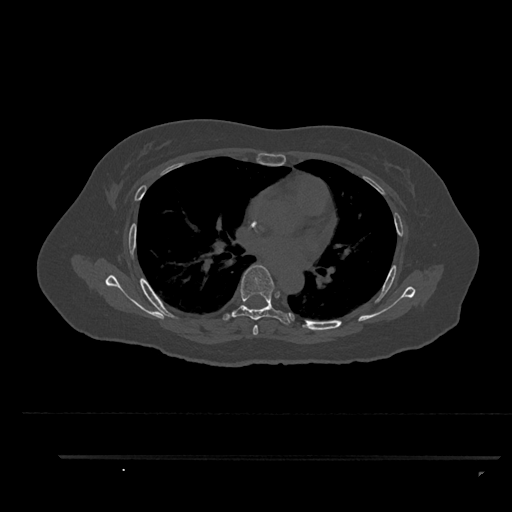
CT including the spine, one axial slice. Position 562 of 797 along the scan axis. Reconstruction kernel Br40s/3. 120 kVp. Bone window (W 1800 / L 400 HU). 512 × 512 image matrix. Female patient, age 44 years. From the clinical record (not read from this slice): primary cancer: renal.
Outlined on this slice (semi-automatic segmentation, software-assisted and operator-edited):
- T5 vertebra: box from (x=253, y=325) to (x=258, y=335) px
- T6 vertebra: (x=222, y=265)–(x=295, y=326)